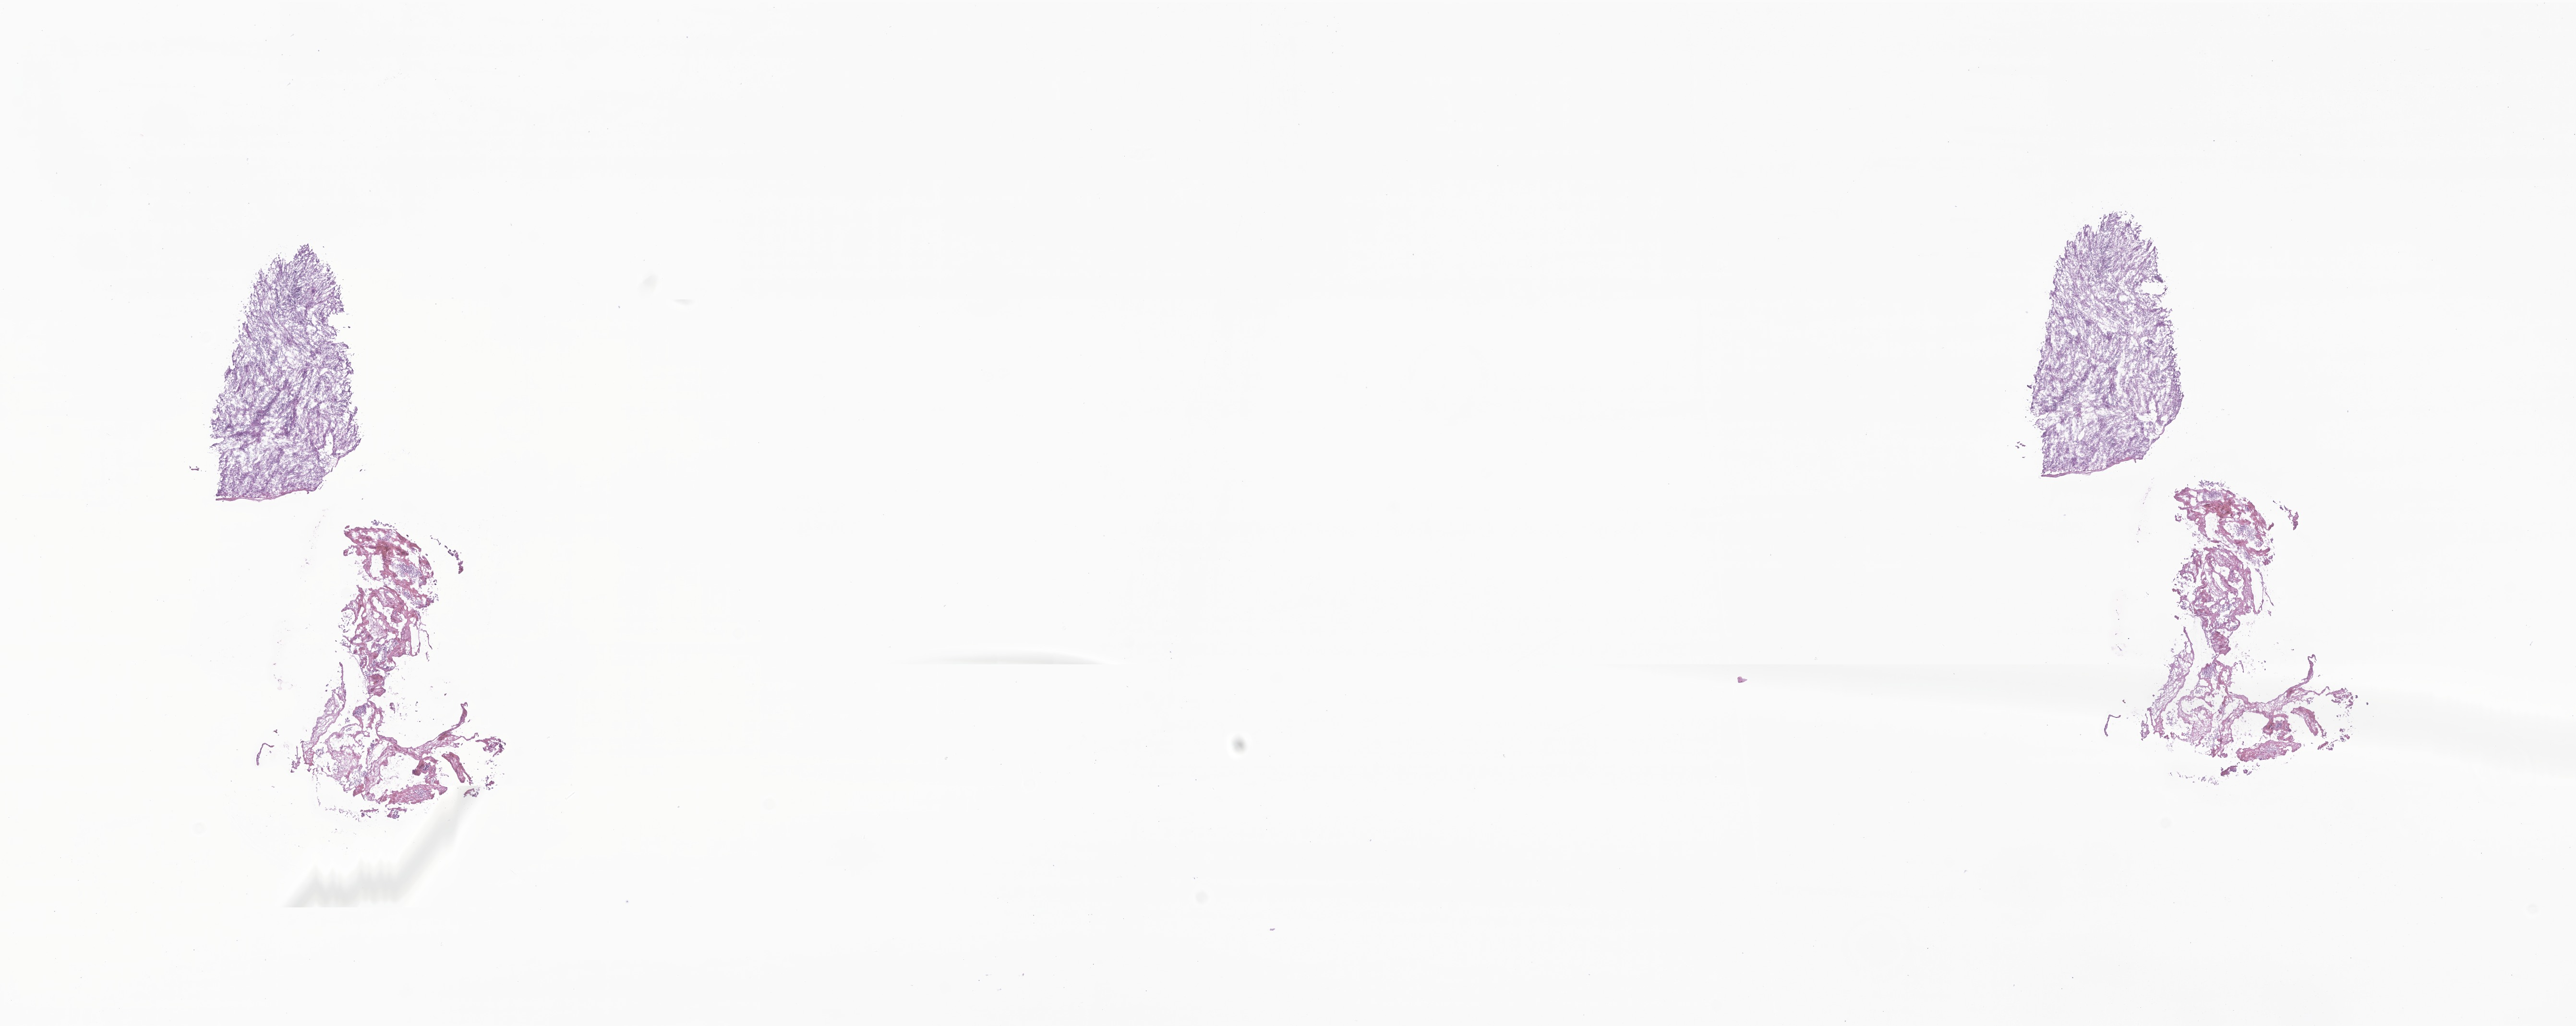
Whole-slide image, hematoxylin and eosin (H&E) stain of tumor tissue from the abdomen — a low-resolution overview of the entire scanned area, about 22.6 x 9.0 mm; cryosection (OCT / tissue freezing medium). Male patient, age 134 months (11 years 2 months).
* diagnosis: Myofibroblastic tumor, NOS